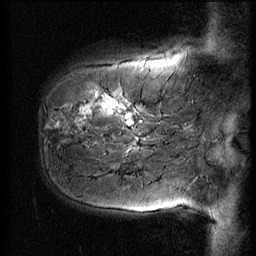
Breast MRI (dynamic contrast-enhanced), one sagittal slice; position 12 of 56 along the scan axis; 3 images stored at this slice position (order not interpretable as contrast timing); 1.5 T; TE 4.2 ms, TR 9 ms; 2.5 mm slice thickness; 256 × 256 image matrix, field of view 180 × 180 mm. Patient: female, 51 years. Case-level facts recorded for this patient, not image findings: setting: breast cancer imaged before/during neoadjuvant chemotherapy; receptor status: HR-positive, HER2-negative.
Structures marked on this image (semi-automatic segmentation, software-assisted and operator-edited):
- analysis volume of interest (the breast-tissue region the enhancement analysis was run in; not a lesion): bounding box <41,58,167,161> (left, top, right, bottom; pixels)
- tumour enhancement mask (voxels above the 140 % enhancement threshold inside the analysis volume of interest): <80,93,141,126>